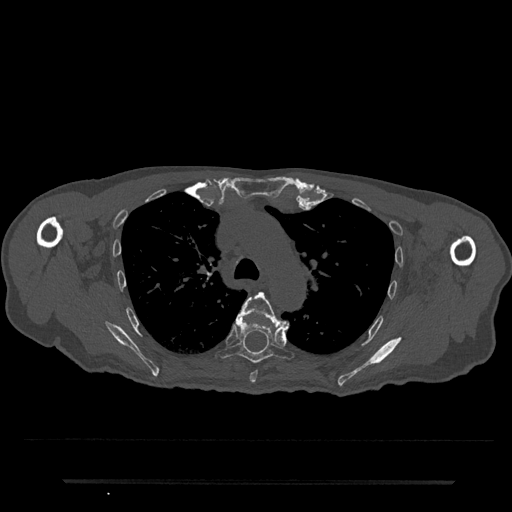
CT including the spine, one axial slice. Slice 546 of 797 in the series (ordered by position). Reconstruction kernel Br40s/3. 120 kVp. Bone window (W 1800 / L 400 HU). 512 × 512 image matrix, field of view 427 × 427 mm. Patient: male, 74 years. From the clinical record (not read from this slice): primary cancer: prostate.
Annotated regions visible in this slice (semi-automatically segmented with operator editing):
- T5 vertebra: bounding box (x1, y1, x2, y2) in pixels: (238, 292, 289, 383)
- T6 vertebra: (216, 315, 295, 364)